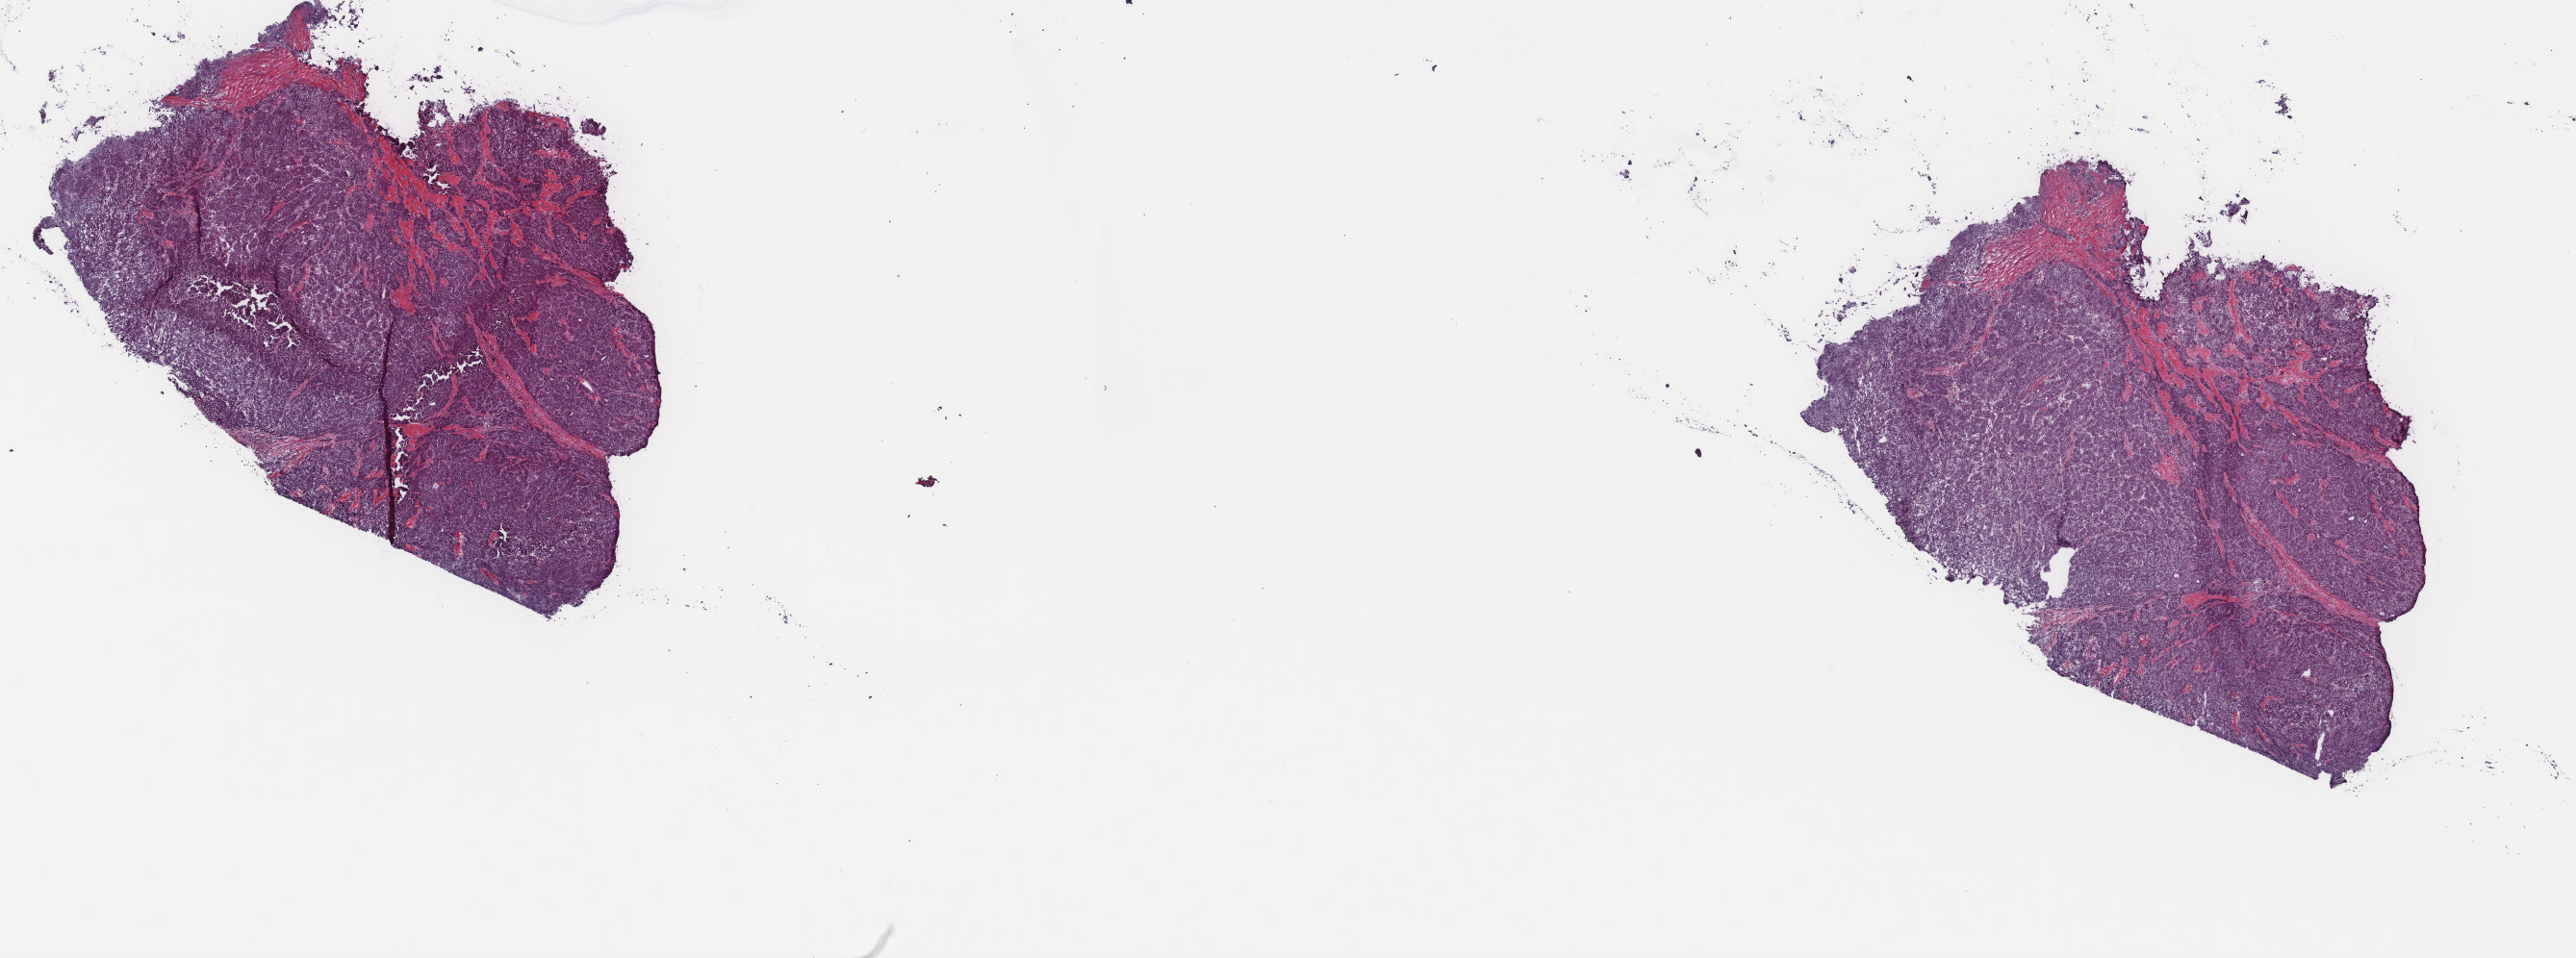
Hematoxylin and eosin (H&E) stained whole-slide image — low-resolution overview of the scanned area, about 21.2 x 7.9 mm (slide scanned at 40x). Frozen section. Primary tumour sample from the liver. Male, age 76 years at initial diagnosis. Histologic grade: G2 (moderately differentiated). Slide review estimates, as recorded: tumour cells 85%, tumour nuclei 90%, normal cells 0%, stromal cells 15%, necrosis 0%. Infiltration values recorded for this section: lymphocyte infiltration 2%, monocyte infiltration 0%, neutrophil infiltration 0%.
AJCC pathologic stage: I (7th edition). Pathologic diagnosis: Hepatocellular carcinoma, NOS.